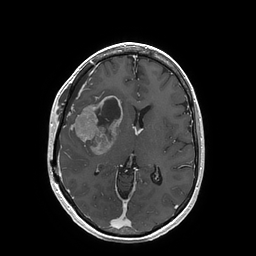
Brain MRI from a brain-tumour surgery series, one axial slice; slice 85 of 202 in the series (ordered by position); T1-weighted post-contrast; 1 mm slice thickness; 256 × 256 image matrix, field of view 250 × 250 mm. Case-level facts recorded for this patient, not image findings: histopathology: Glioblastoma; WHO grade: 4; IDH mutation: no.
Annotated regions visible in this slice (manually delineated by an expert):
- tumour: bounding box [x1, y1, x2, y2] px = [73, 96, 123, 155]